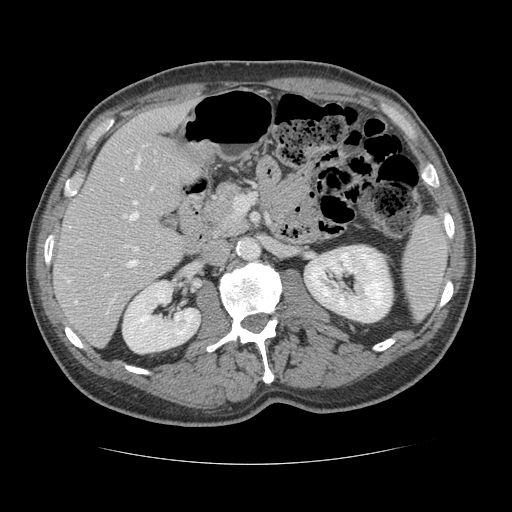
Contrast-enhanced abdominal CT, one axial slice; position 66 of 134 along the scan axis; reconstruction kernel STANDARD; intravenous contrast given; soft-tissue window (W 400 / L 40 HU); 2.5 mm slice thickness; 512 × 512 image matrix, field of view 377 × 377 mm. Male patient, age 68 years. Case-level facts recorded for this patient, not image findings: diagnosis: colorectal cancer liver metastases, imaged before liver resection; multiple liver metastases: yes.
Annotated regions visible in this slice (manually delineated by an expert):
- hepatic veins: box from (x=68, y=157) to (x=153, y=303) px
- liver: (x=55, y=106)–(x=203, y=345)
- planned liver remnant (the part of the liver to remain after resection): (x=55, y=105)–(x=203, y=335)
- portal vein (with intrahepatic branches): (x=123, y=214)–(x=137, y=267)